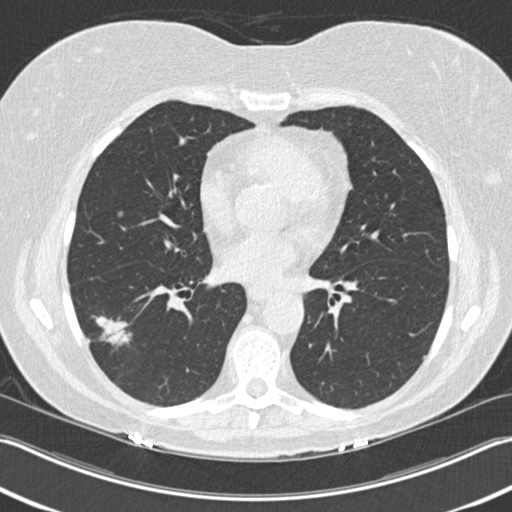
Chest CT (low-dose screening protocol), one axial image, baseline annual screen, lung window (W 1500 / L -600 HU), 2 mm slice thickness, standard (soft-tissue) reconstruction kernel (B30f), slice 102 of 211 in the series. Female, age 63 years at enrolment.
Lesion marked by an expert reader, bounding box <70,309,135,370> (left, top, right, bottom; pixels). The screening reader recorded 3 non-calcified nodules or masses ≥4 mm on this exam (right upper lobe, right lower lobe, right lower lobe); which of them this box marks is not recorded. Official screen result: positive, change unspecified: nodule(s) >= 4 mm or enlarging nodule(s), mass(es), or other non-specific abnormalities suspicious for lung cancer.